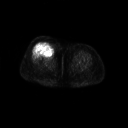
FDG PET of an extremity soft-tissue mass (from a PET/CT study), one axial slice. Position 33 of 267 along the scan axis. 128 × 128 image matrix, field of view 700 × 700 mm. Female patient, age 56 years. Case-level facts recorded for this patient, not image findings: histological type: malignant solitary fibrous tumor; grade: intermediate; site of the primary tumour: right thigh.
Annotated regions visible in this slice (expert contour drawn on MRI and transferred to this co-registered scan by the dataset authors):
- gross tumour volume including surrounding oedema: box from (x=34, y=41) to (x=55, y=59) px
- gross tumour volume (mass): (x=35, y=41)–(x=55, y=58)